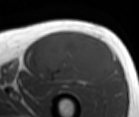
MRI of an extremity soft-tissue mass, one axial slice; position 55 of 86 along the scan axis; MR volume resampled by the dataset authors to the PET/CT grid (not the native acquisition matrix); 139 × 117 image matrix. Male patient. Case-level facts recorded for this patient, not image findings: histological type: extraskeletal osteosarcoma; grade: high; site of the primary tumour: thigh.
Structures marked on this image (expert contour drawn on MRI and transferred to this co-registered scan by the dataset authors):
- gross tumour volume (mass): box from (x=36, y=30) to (x=114, y=83) px